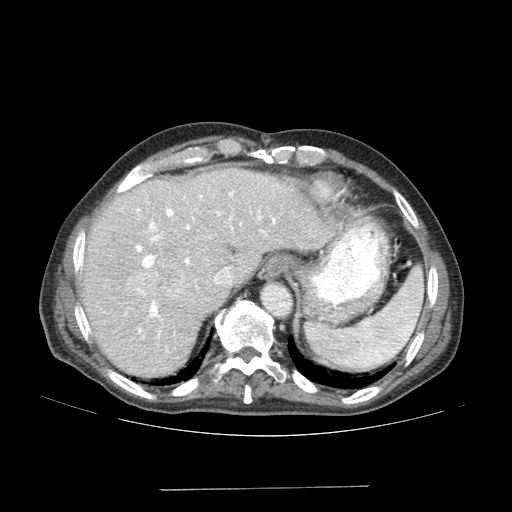
Contrast-enhanced abdominal CT (liver protocol), one axial slice; slice 126 of 192 in the series (ordered by position); reconstruction kernel SOFT; soft-tissue window (W 400 / L 40 HU); 2.5 mm slice thickness; 512 × 512 image matrix, field of view 400 × 400 mm. From the clinical record (not read from this slice): diagnosis: hepatocellular carcinoma (patient treated with transarterial chemoembolisation; whether this scan precedes or follows treatment is not stated here); TNM stage (as recorded): Stage-IVA; Child-Pugh class: A; tumour differentiation: poorly differentiated.
Annotated regions visible in this slice (semi-automatic segmentation, software-assisted and operator-edited):
- liver parenchyma outside the tumour (the mass and vessels are separate outlines, so this box may not span the whole liver): bounding box [x1, y1, x2, y2] px = [80, 168, 332, 376]
- mass: [126, 262, 184, 301]
- liver vessels: [125, 192, 276, 338]